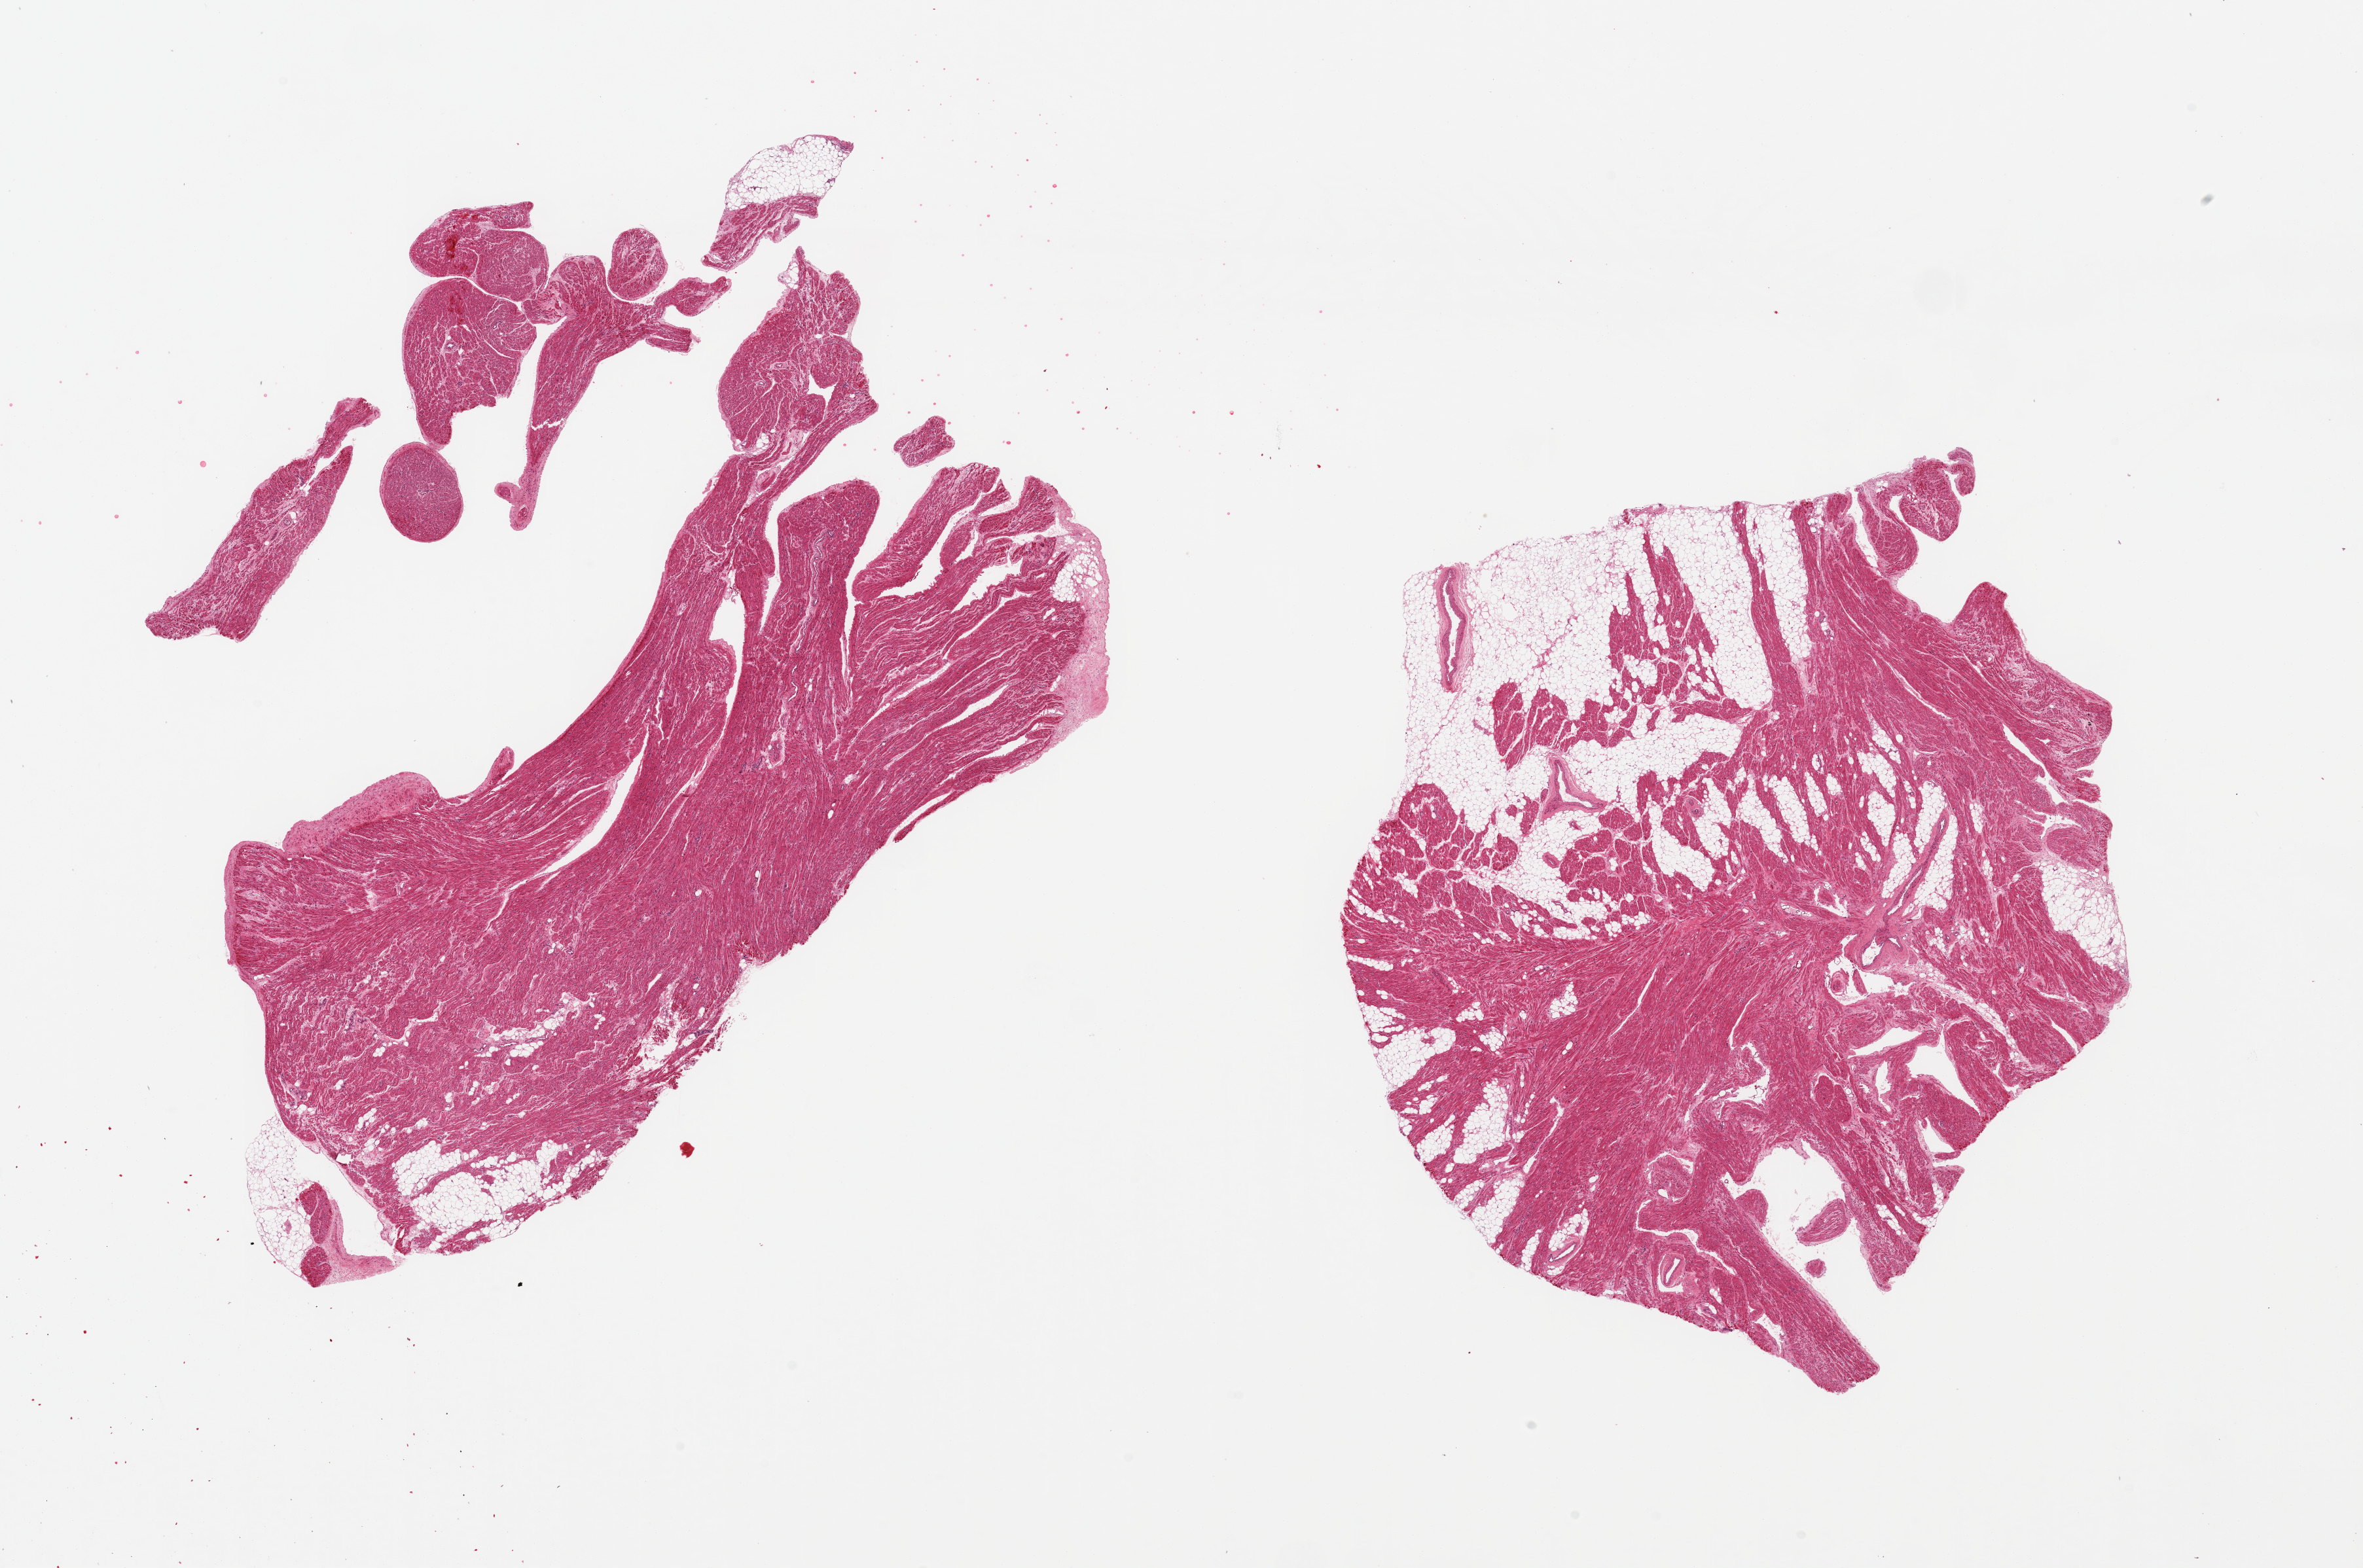
Whole-slide image, H&E stain, brightfield — shown as a low-resolution overview of the whole scanned area (about 28.5 x 18.9 mm, slide scanned at 20x), PAXgene-fixed, paraffin-embedded tissue, sampled site (target tissue): auricular appendage, tissue donor sample.
Reviewer comment on this tissue sample: 2 pieces ~9x6mm, presumed atrium.